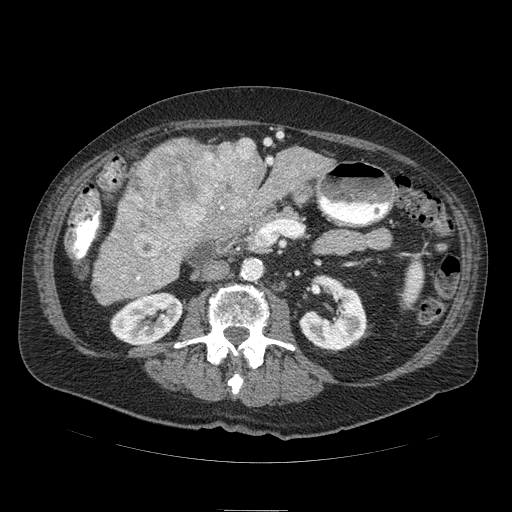
Contrast-enhanced abdominal CT (liver protocol), one axial slice; slice 29 of 103 in the series (ordered by position); soft-tissue window (W 400 / L 40 HU); 2.5 mm slice thickness; 512 × 512 image matrix, field of view 440 × 440 mm. From the clinical record (not read from this slice): diagnosis: hepatocellular carcinoma (patient treated with transarterial chemoembolisation; whether this scan precedes or follows treatment is not stated here); TNM stage (as recorded): Stage-IIIA; Child-Pugh class: B; tumour differentiation: well differentiated; tumour nodularity: multinodular.
Outlined on this slice (semi-automatically segmented with operator editing):
- liver parenchyma outside the tumour (the mass and vessels are separate outlines, so this box may not span the whole liver): box from (x=96, y=138) to (x=334, y=284) px
- mass: (x=121, y=138)–(x=265, y=268)
- liver vessels: (x=267, y=158)–(x=273, y=164)